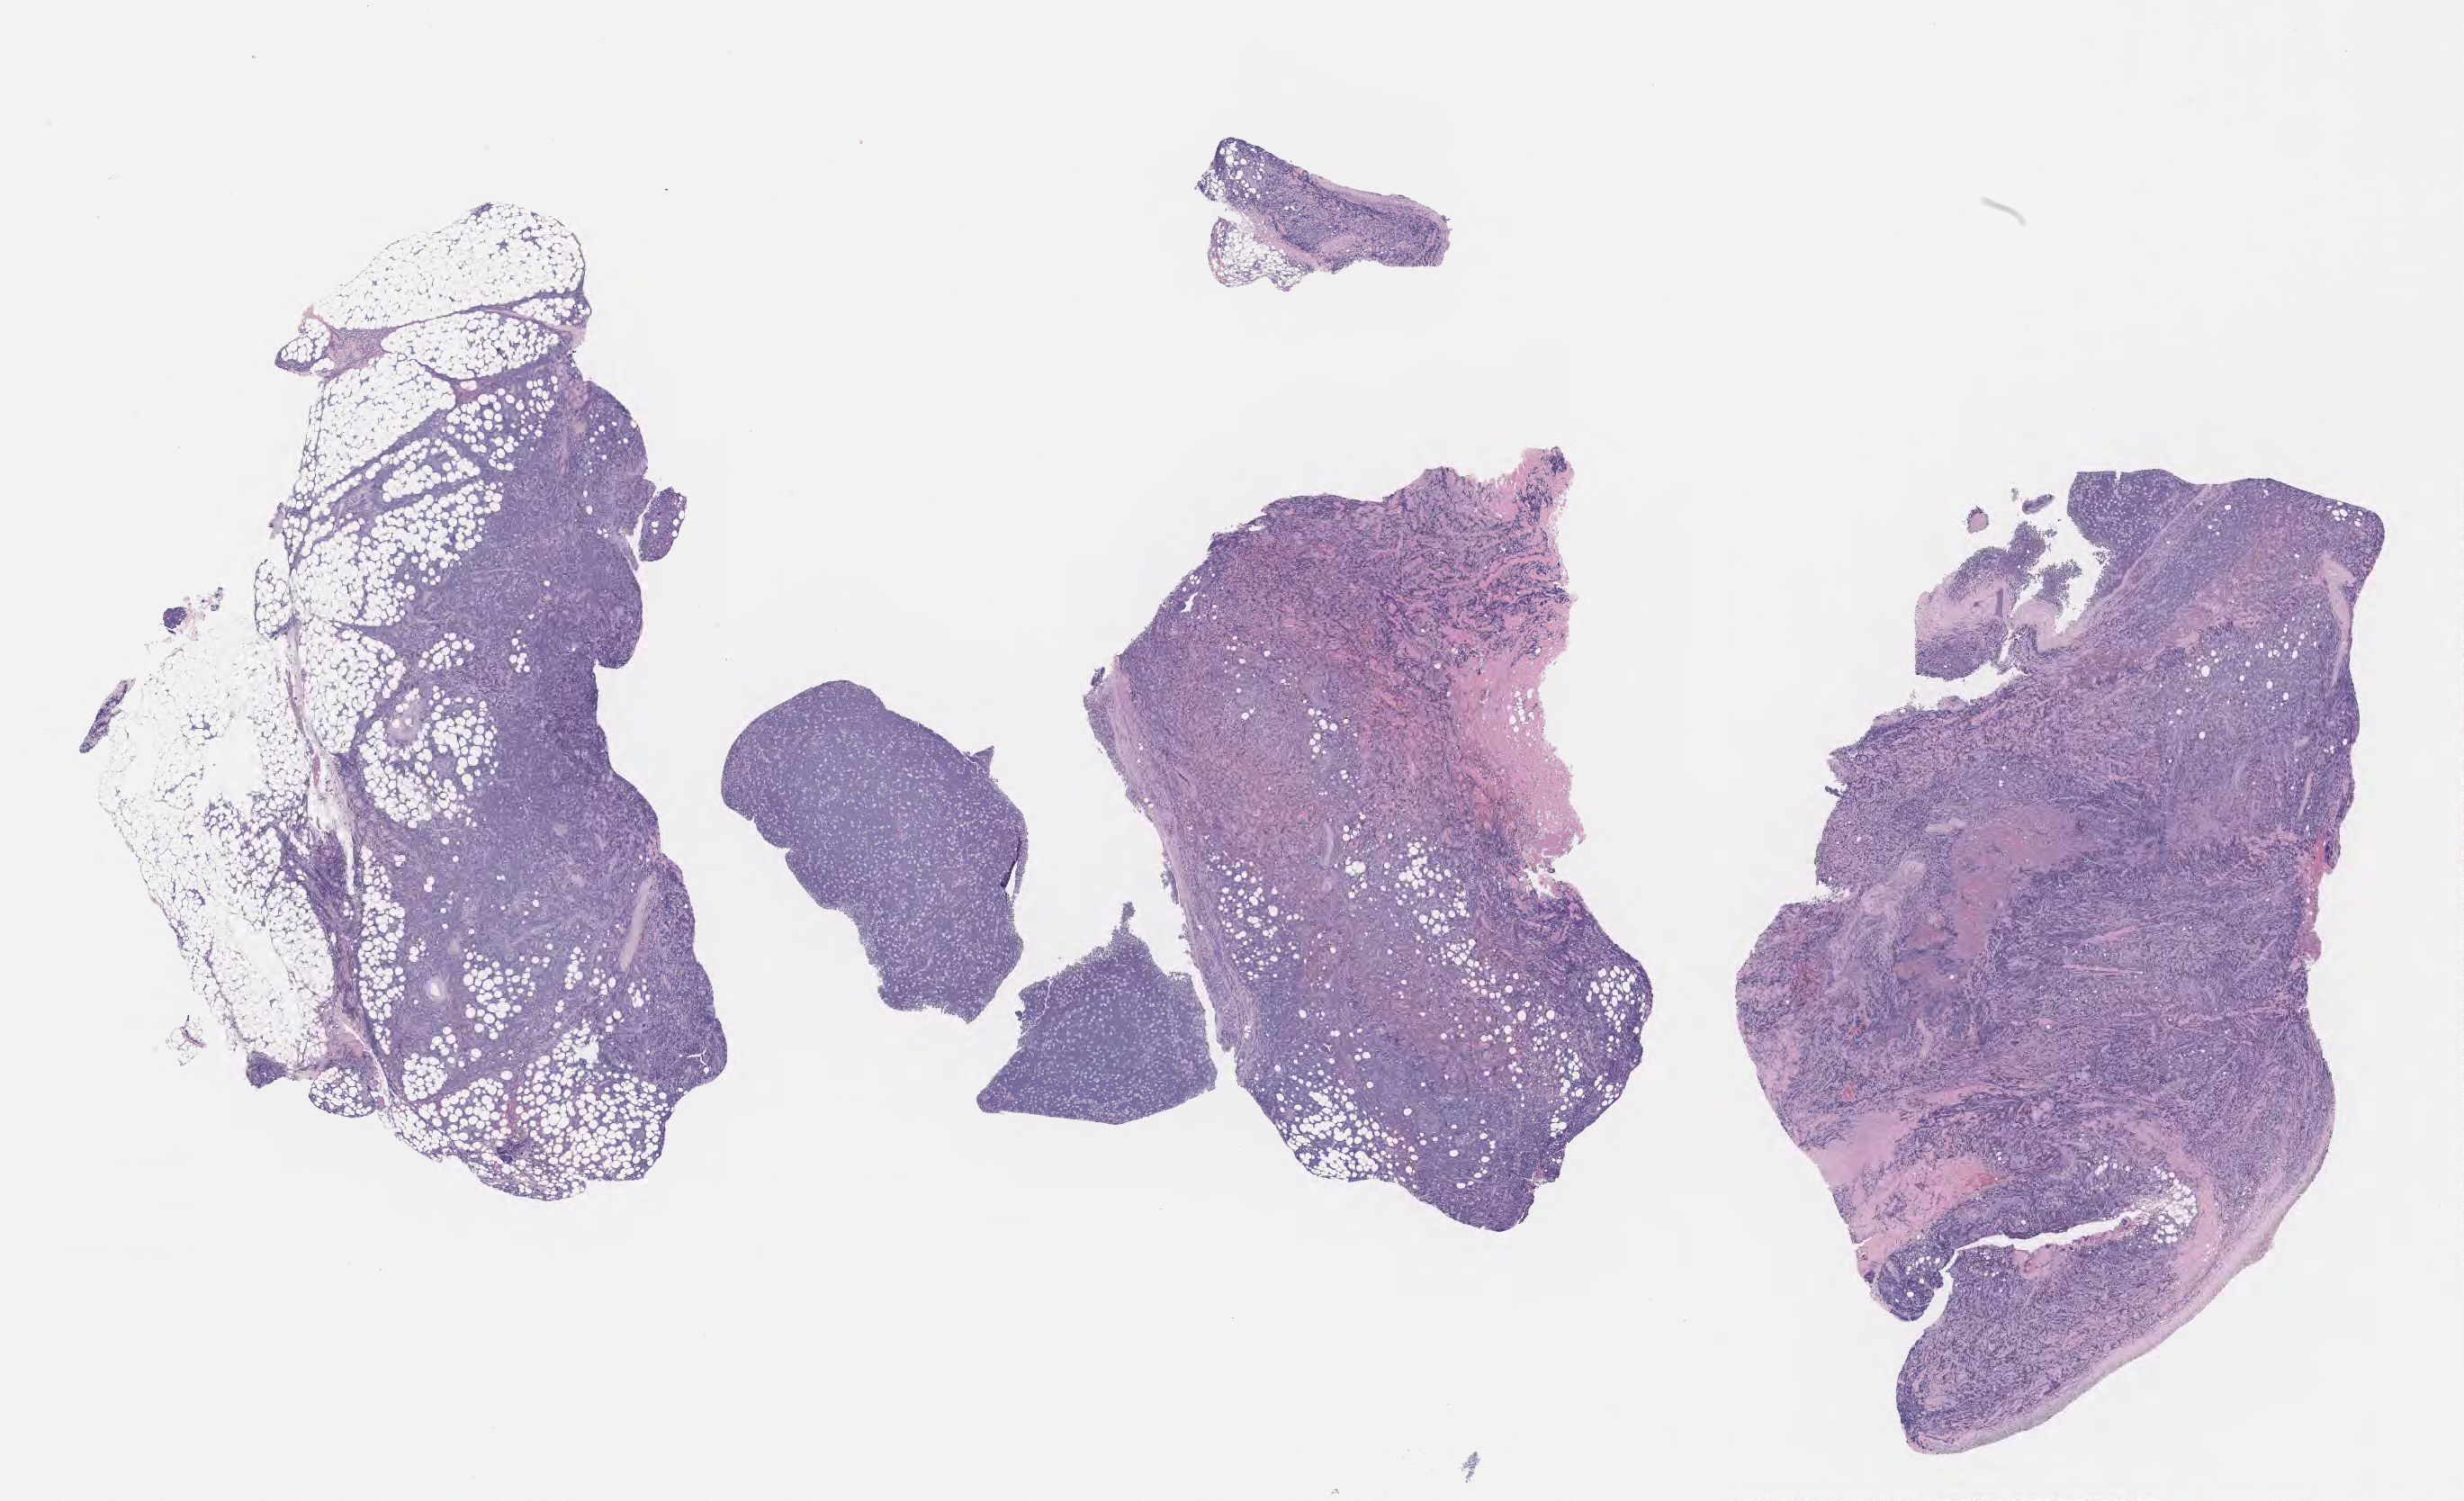
Whole-slide image, H&E stain, shown as a low-resolution overview of the whole scanned area (about 22.1 x 13.5 mm), specimen: tumor tissue, site: head and neck. Male patient, aged 29.
Diagnosis: Burkitt lymphoma, NOS.